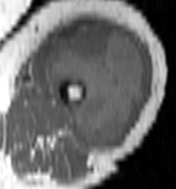
MRI of an extremity soft-tissue mass, one axial slice. Position 58 of 100 along the scan axis. MR volume resampled by the dataset authors to the PET/CT grid (not the native acquisition matrix). 176 × 189 image matrix. Female patient. Case-level facts recorded for this patient, not image findings: histological type: undifferentiated – high grade; grade: high; site of the primary tumour: left thigh.
Structures marked on this image (expert contour drawn on MRI and transferred to this co-registered scan by the dataset authors):
- gross tumour volume including surrounding oedema: bounding box [x1, y1, x2, y2] px = [46, 25, 145, 149]
- gross tumour volume (mass): [46, 25, 145, 149]